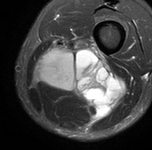
MRI of an extremity soft-tissue mass, one axial slice. Position 32 of 90 along the scan axis. STIR. MR volume resampled by the dataset authors to the PET/CT grid (not the native acquisition matrix). 3.27 mm slice thickness. 152 × 150 image matrix, field of view 148 × 146 mm. Male patient. Case-level facts recorded for this patient, not image findings: histological type: undifferentiated pleomorphic liposarcoma; grade: high; site of the primary tumour: left thigh.
Outlined on this slice (expert contour drawn on MRI and transferred to this co-registered scan by the dataset authors):
- gross tumour volume including surrounding oedema: bounding box [x1, y1, x2, y2] px = [34, 41, 122, 122]
- gross tumour volume (mass): [43, 55, 112, 106]